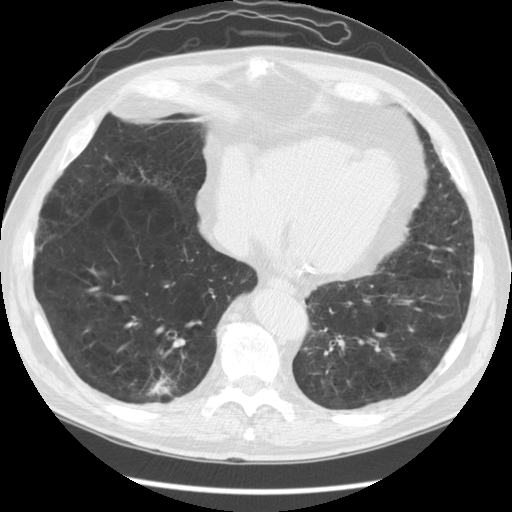
Low-dose screening chest CT, axial slice. First (baseline) screen. Lung window (W 1500 / L -600 HU). 2.5 mm slice thickness. Slice 97 of 141 in the series. 512 × 512 image matrix. Male, age 67 years at enrolment. Former smoker at enrolment.
Expert-annotated lung lesion, bounding box [x1, y1, x2, y2] px = [120, 356, 186, 416]. The screening reader recorded 2 non-calcified nodules or masses ≥4 mm on this exam (right lower lobe, right lower lobe); which of them this box marks is not recorded. Participant outcome: lung cancer diagnosed 78 days after this screen — squamous cell carcinoma, NOS, right lower lobe, moderately differentiated (G2), stage IA (AJCC 6th edition), 23 mm at pathology.